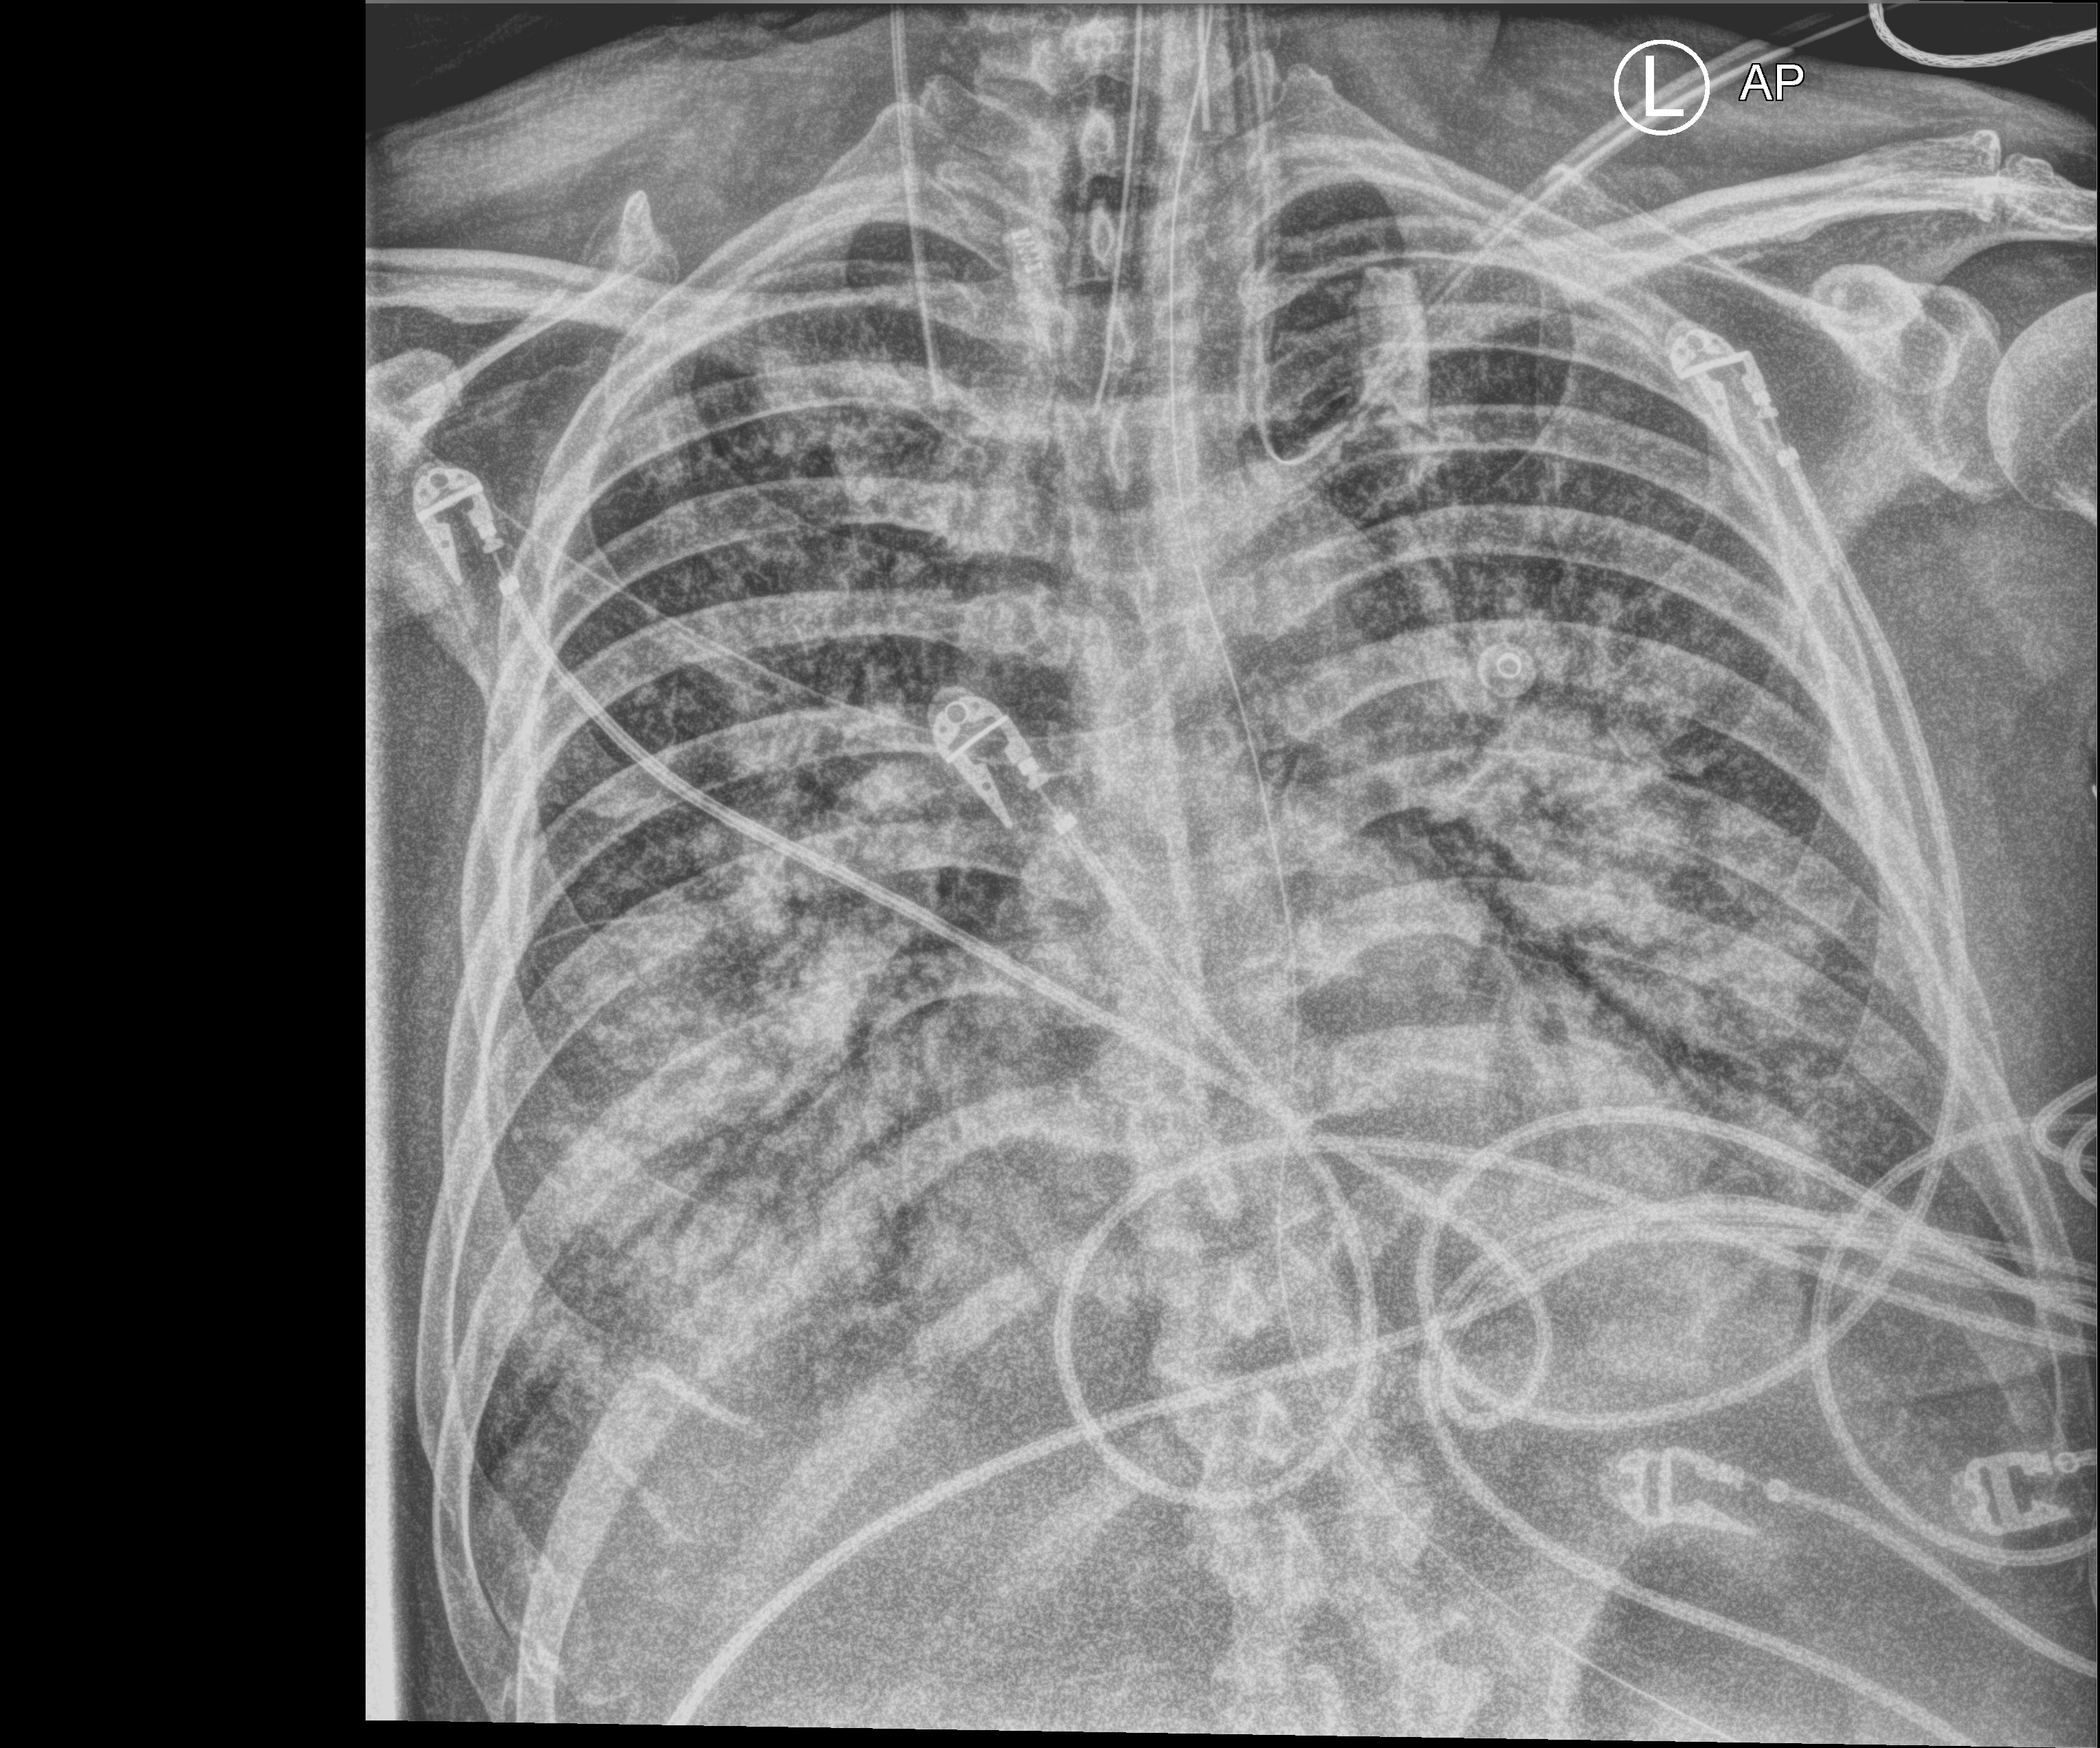
Chest X-ray (portable); anteroposterior (AP) projection. Male patient hospitalised with COVID-19, age 60–74 years.
Hospital-stay facts (about this admission, not read from this image; timing relative to this image not recorded):
- mechanically ventilated during this hospital stay: yes
- admitted to intensive care during this hospital stay: yes